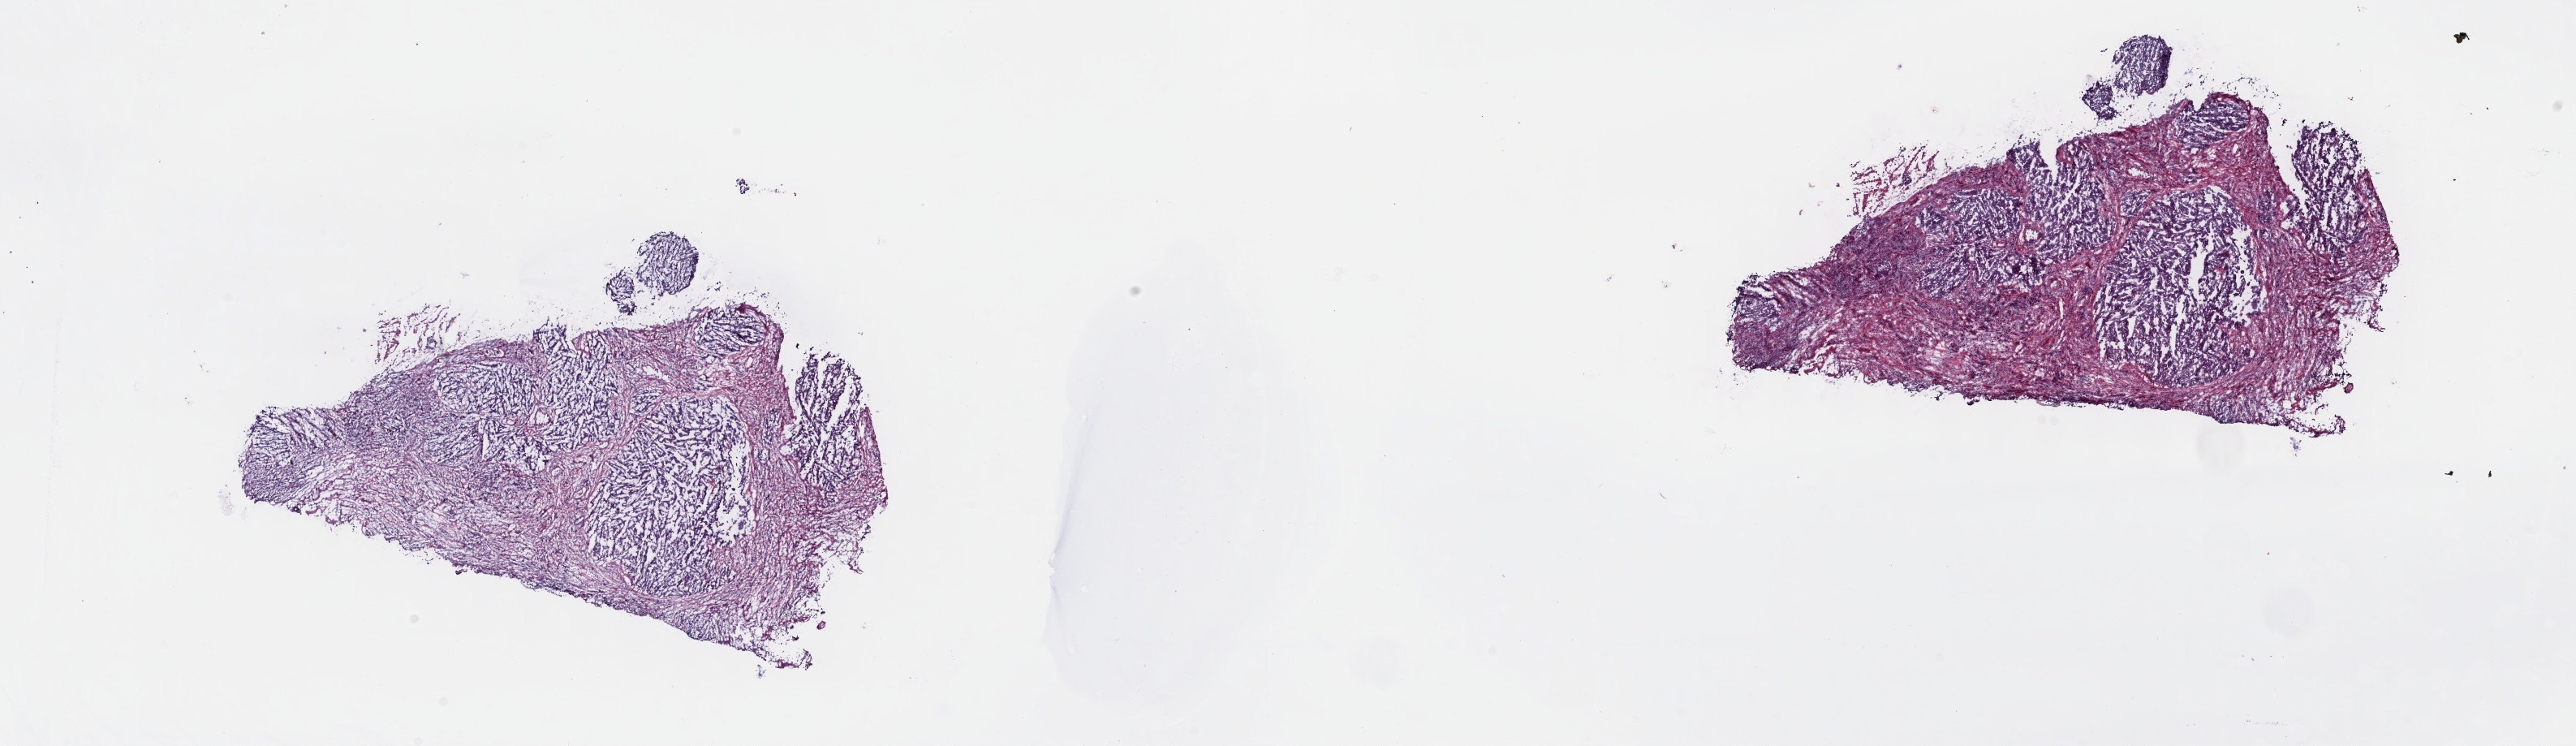
Digitized Hematoxylin and eosin (H&E) stained tissue section (whole slide), whole scanned area (about 25.7 x 7.4 mm, acquisition: 40x scan) shown as a low-resolution overview, frozen section from the top of the tissue portion, primary tumour sample from the testis. Male patient; age at initial diagnosis 26 years. Pathologist review of this section (percent, as recorded): tumour cells 70%, tumour nuclei 70%, normal cells 0%, stromal cells 20%, necrosis 10%. Infiltration values recorded for this section: lymphocyte infiltration 70%, monocyte infiltration 10%, neutrophil infiltration 10%.
Diagnosis: Embryonal carcinoma, NOS. Laterality: left. AJCC pathologic stage: II (4th edition).